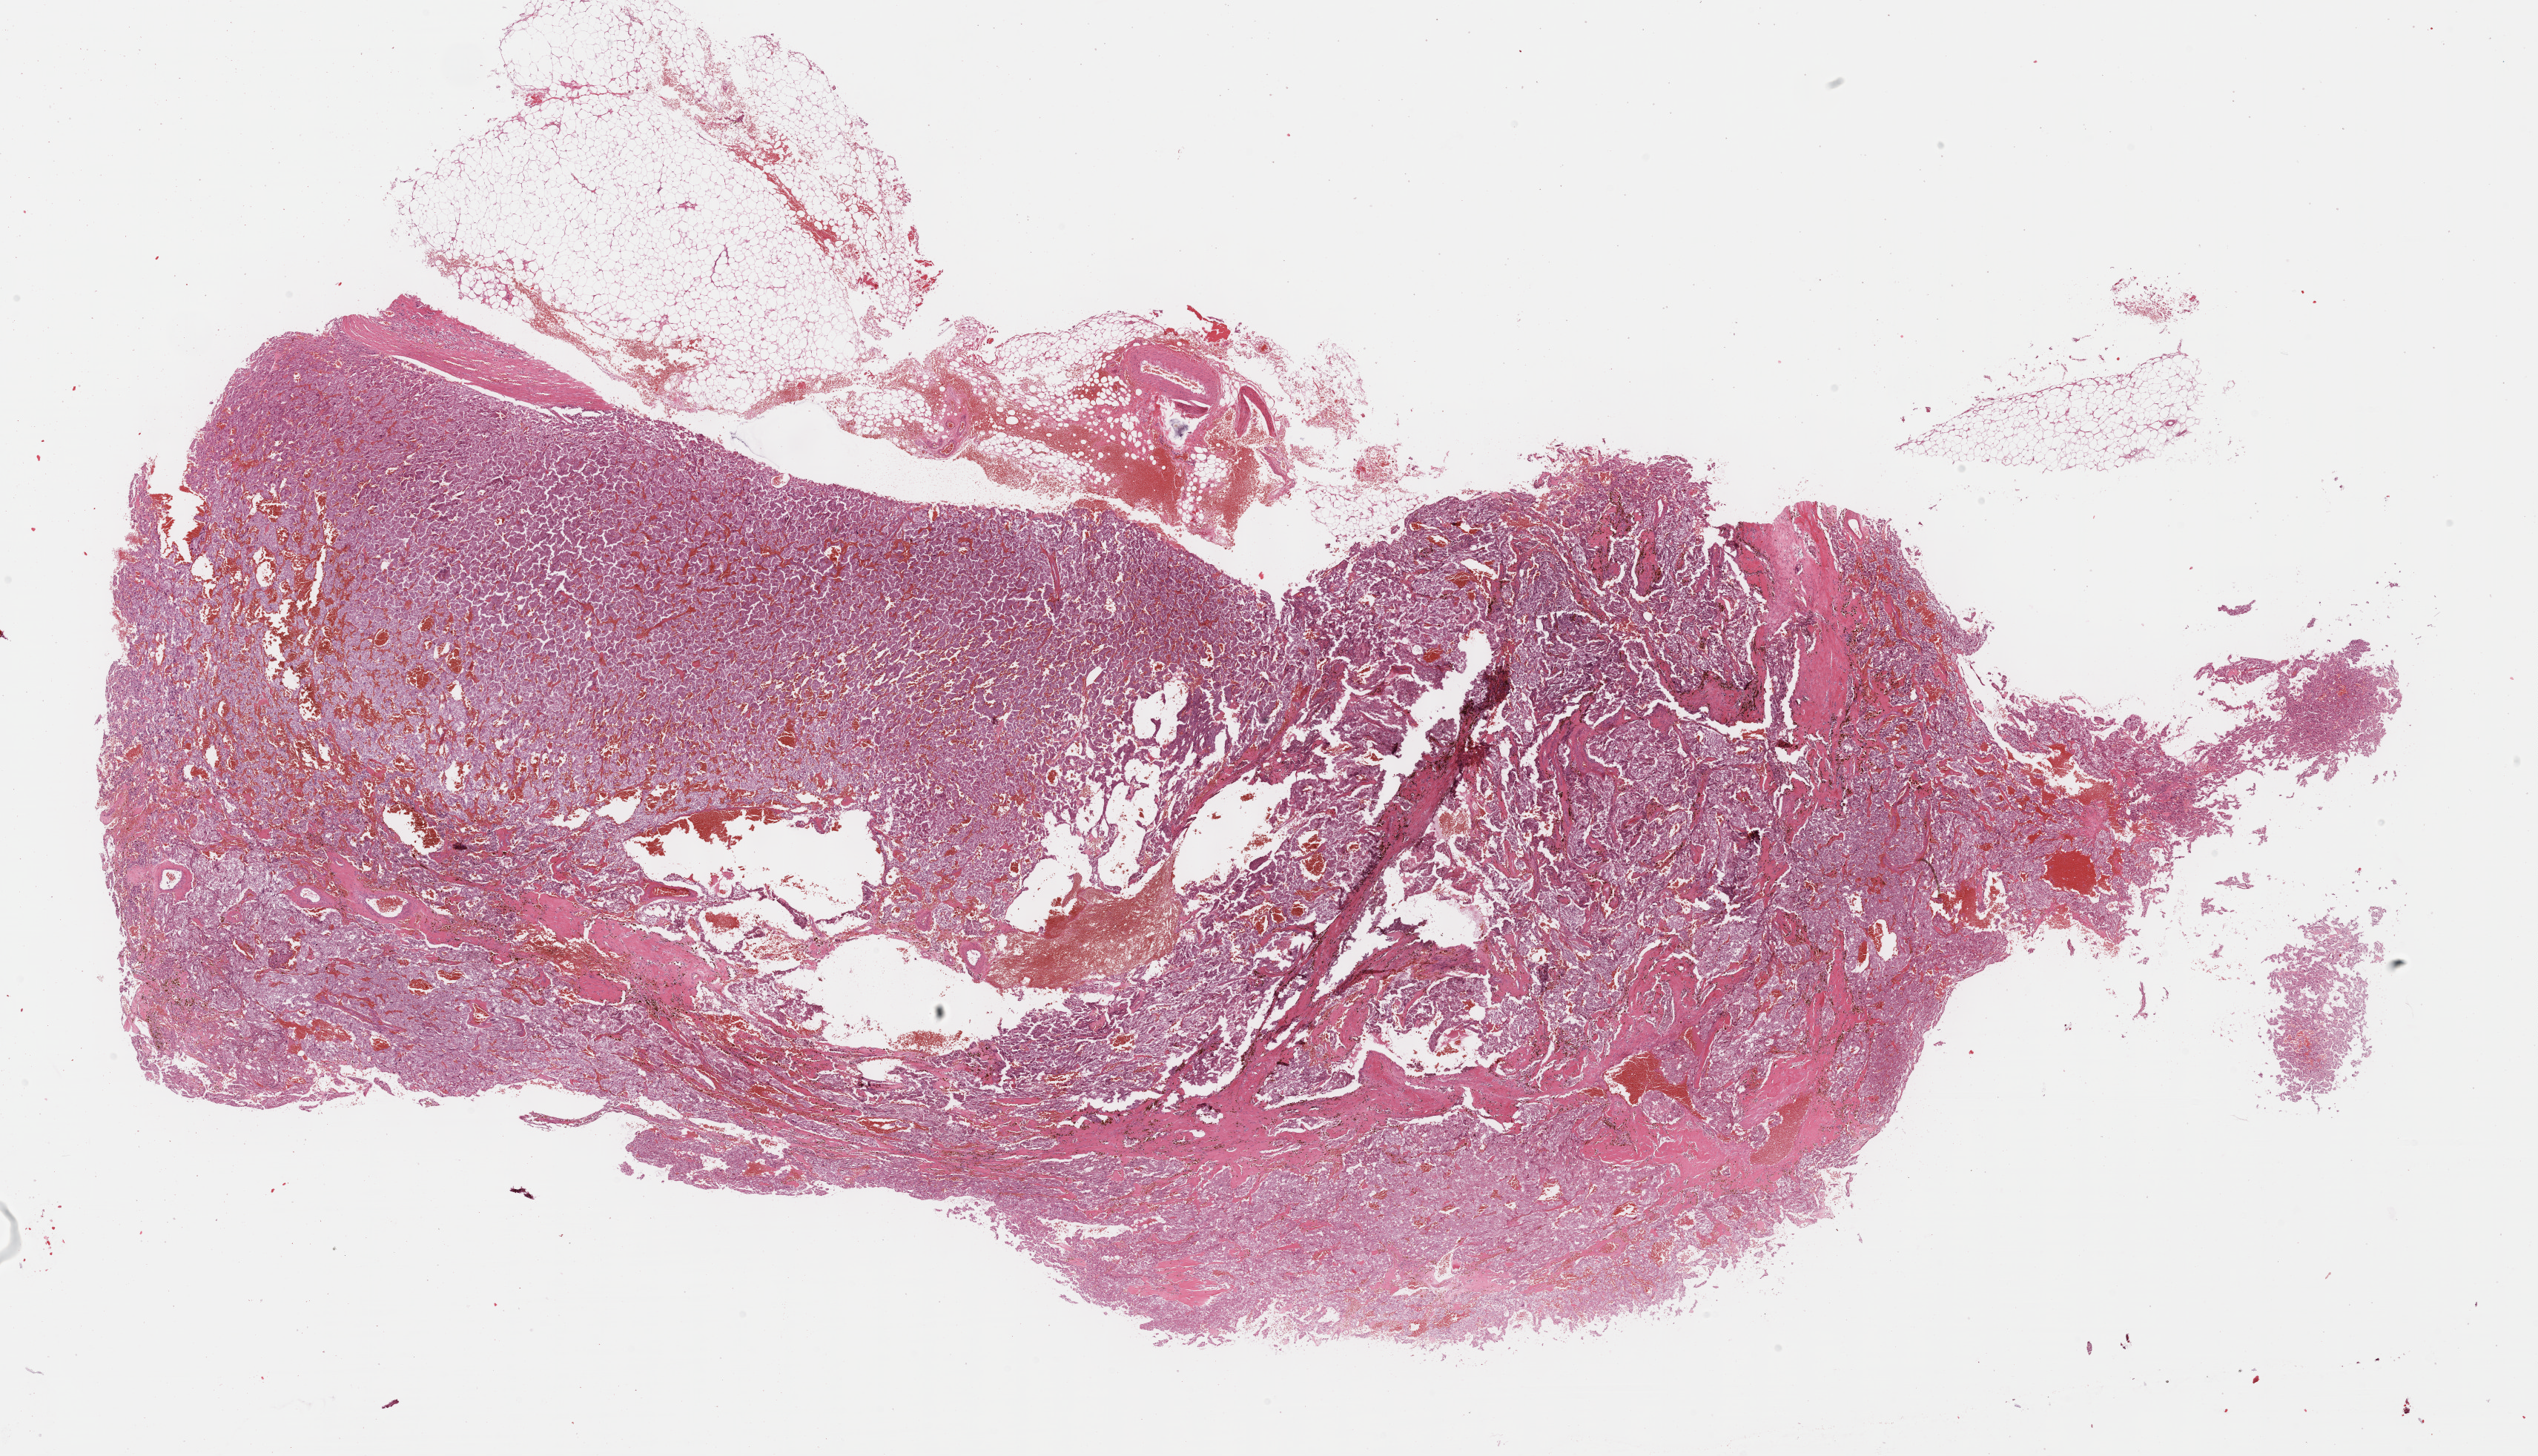
Whole-slide histology image, H&E-stained — shown as a low-resolution overview of the whole scanned area (about 27.7 x 15.9 mm, acquisition: 40x scan). Formalin-fixed paraffin-embedded (FFPE) diagnostic section. Adrenal gland, primary tumour sample. Patient: female, age at initial diagnosis 57 years.
Histologic diagnosis: Pheochromocytoma, NOS.